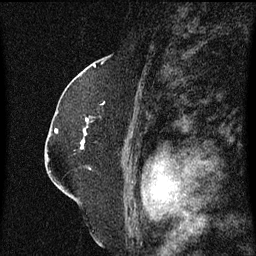
Breast MRI (dynamic contrast-enhanced), one sagittal slice; slice 41 of 60 in the series (ordered by position); dynamic contrast-enhanced series, image 2 of 3 at this slice position (ordered by acquisition); 1.5 T; TE 4.2 ms, TR 8.4 ms; 2 mm slice thickness; 256 × 256 image matrix, field of view 200 × 200 mm. Female patient, age 52 years. Case-level facts recorded for this patient, not image findings: setting: breast cancer imaged before/during neoadjuvant chemotherapy; receptor status: HR-positive, HER2-negative.
Outlined on this slice (semi-automatic segmentation, software-assisted and operator-edited):
- analysis volume of interest (the breast-tissue region the enhancement analysis was run in; not a lesion): bounding box (x1, y1, x2, y2) in pixels: (81, 104, 104, 151)
- tumour enhancement mask (voxels above the 70 % enhancement threshold inside the analysis volume of interest): (81, 128, 88, 149)